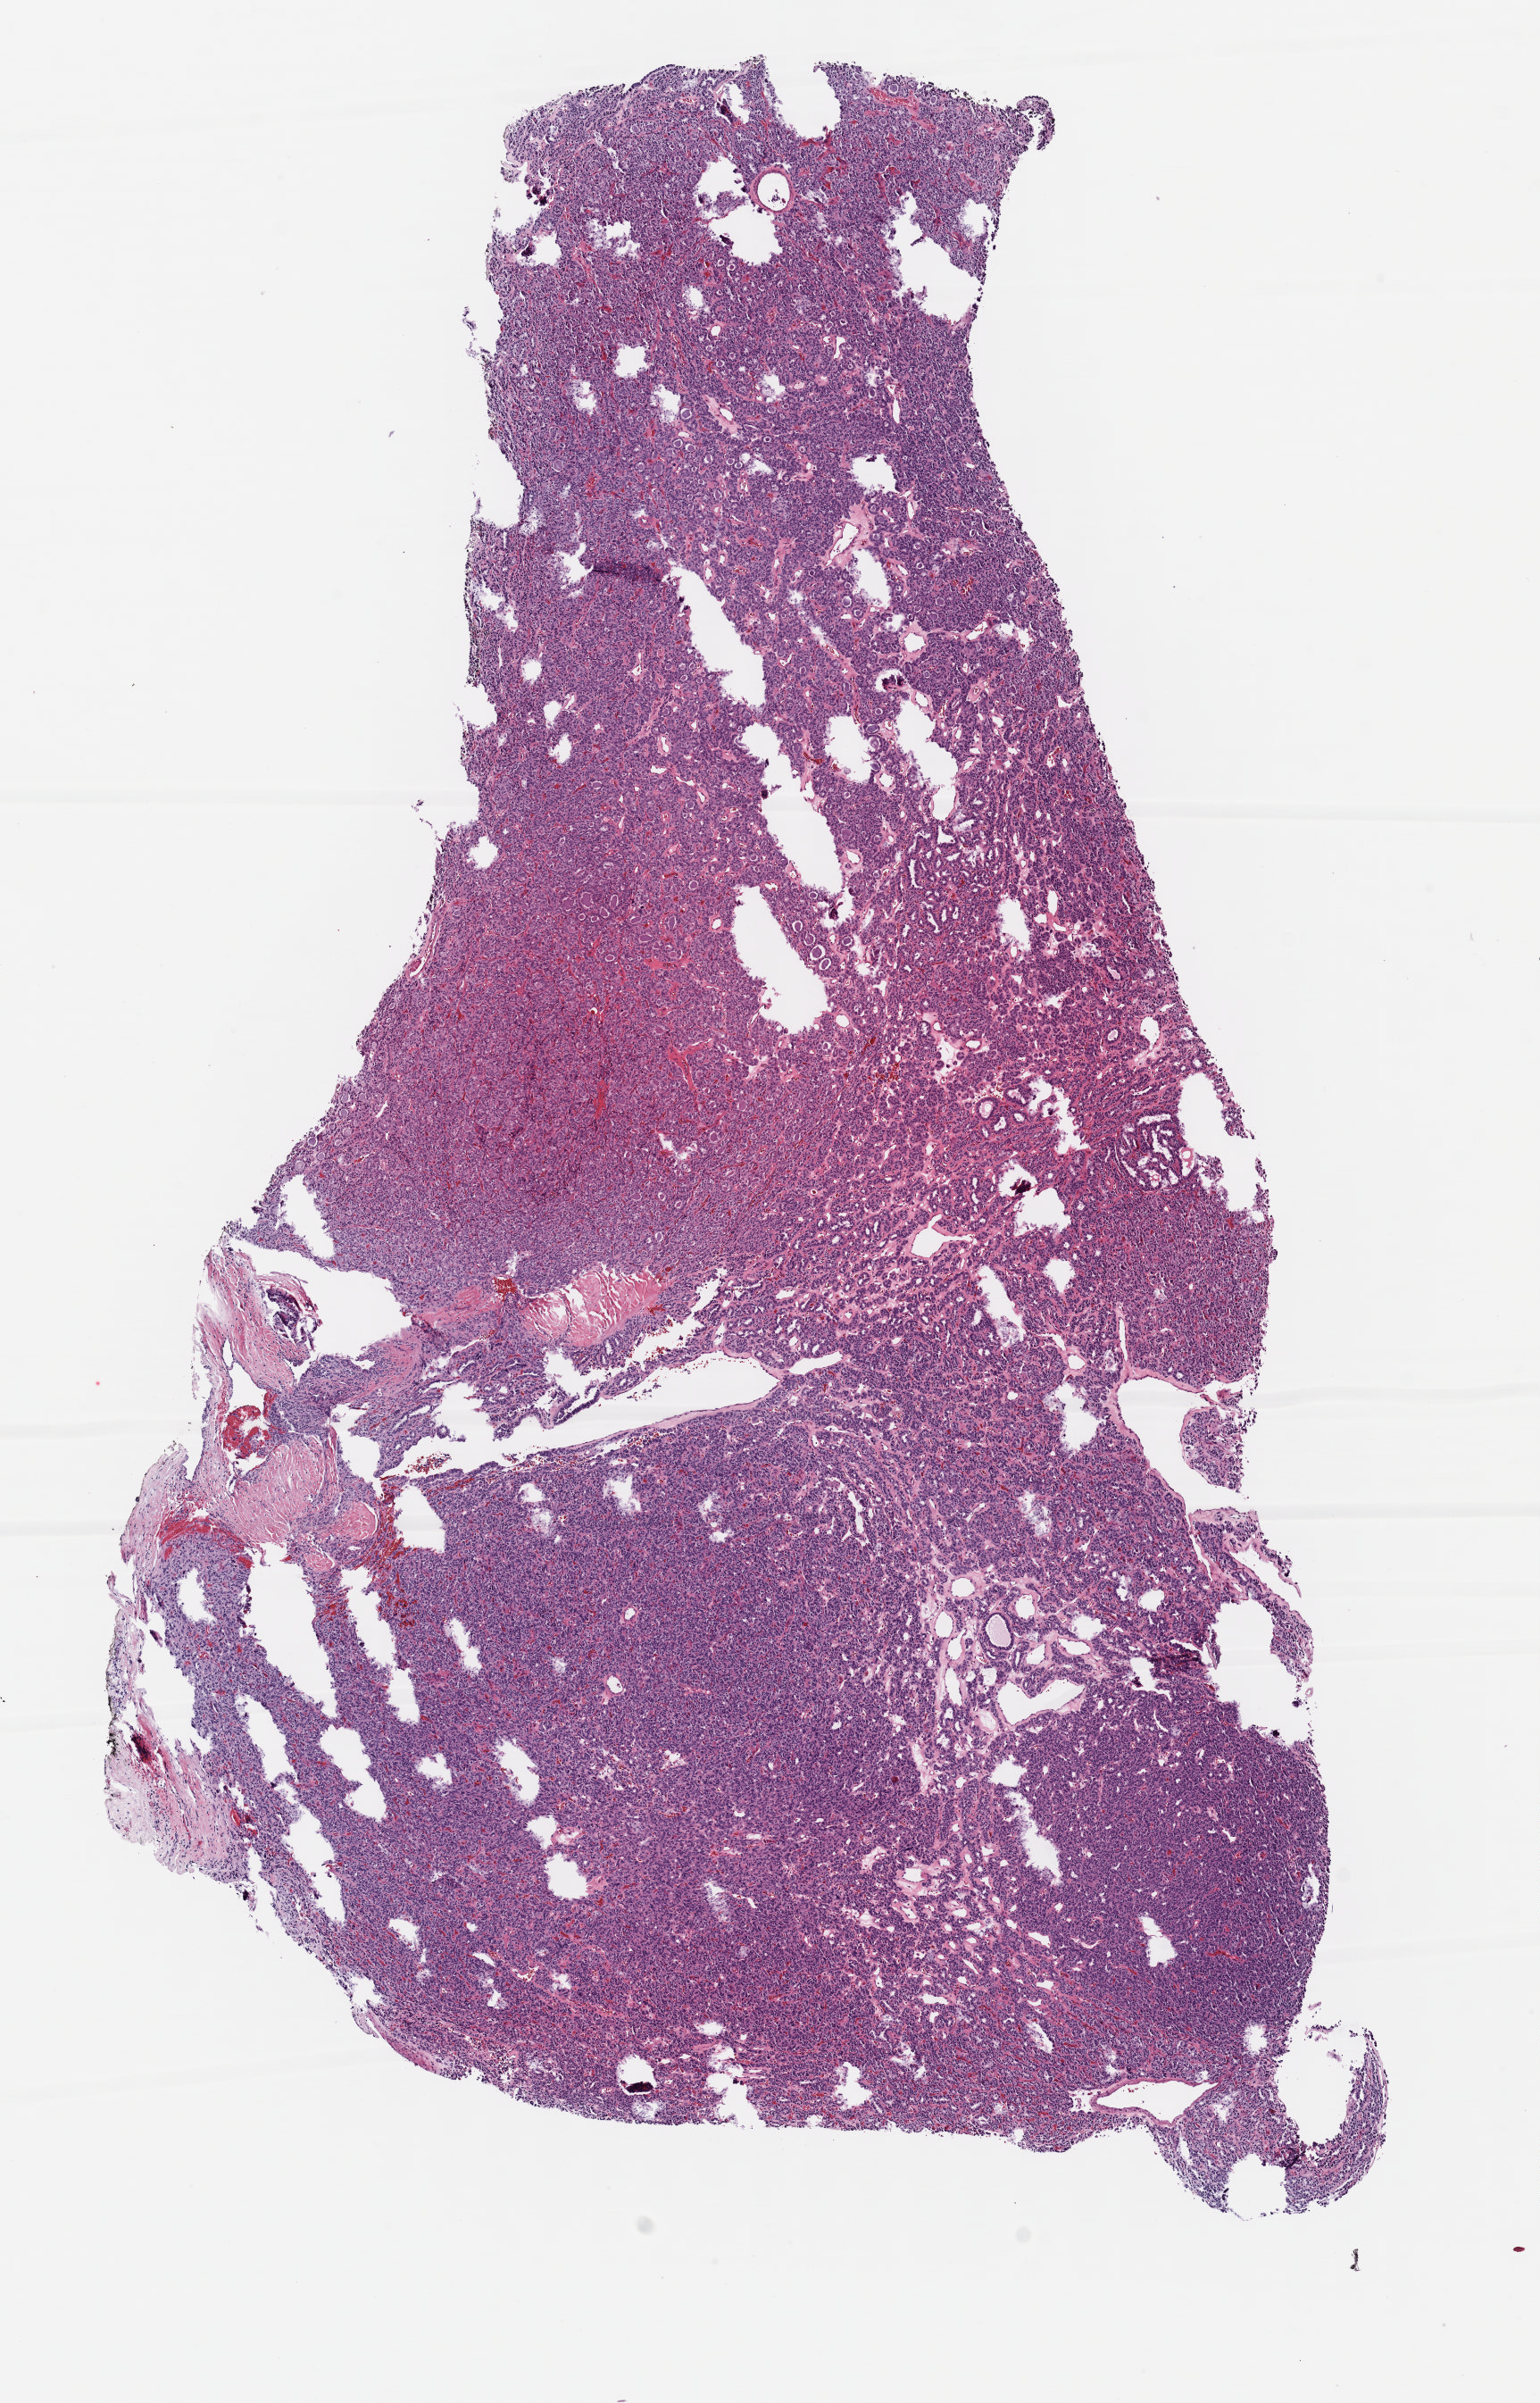
H&E-stained whole-slide image, a low-resolution overview of the entire scanned area, about 6.8 x 10.6 mm. FFPE section. Primary tumour sample from the thyroid. Male patient; age at initial diagnosis 25 years.
TNM: T2 N1b MX. Diagnosis: Papillary adenocarcinoma, NOS (thyroid gland). AJCC pathologic stage: I (7th edition). Lymph nodes positive (case pathology): 11 of 14 examined.